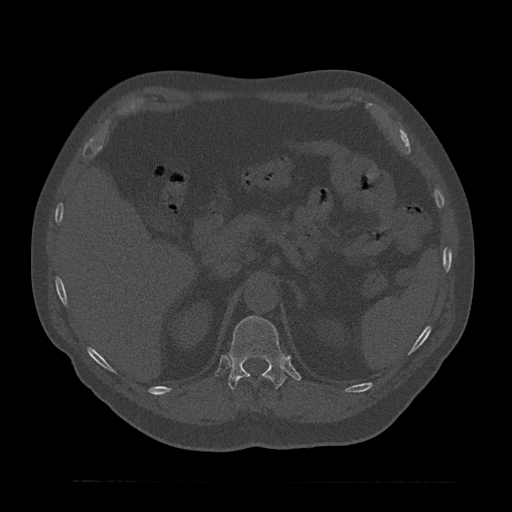
CT including the spine, one axial slice. Slice 243 of 797 in the series (ordered by position). Reconstruction kernel Br40s/3. 120 kVp. Bone window (W 1800 / L 400 HU). 512 × 512 image matrix, field of view 430 × 430 mm. Patient: male, 61 years. From the clinical record (not read from this slice): primary cancer: prostate.
Outlined on this slice (semi-automatically segmented with operator editing):
- T12 vertebra: bounding box <228,316,286,391> (left, top, right, bottom; pixels)